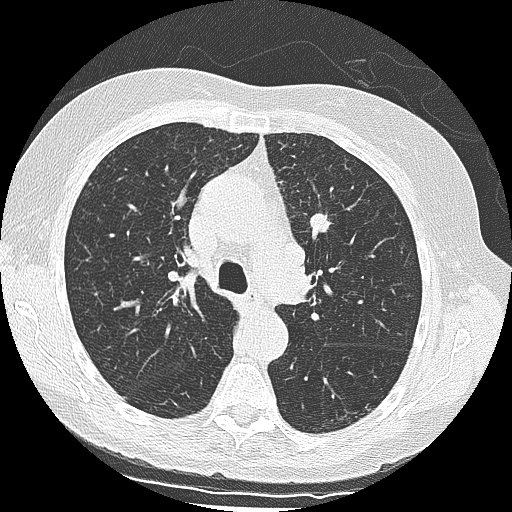
Low-dose screening chest CT, one axial slice; position 95 of 139 along the scan axis; reconstruction kernel LUNG; lung window (W 1500 / L -600 HU); 2.5 mm slice thickness; 512 × 512 image matrix, field of view 318 × 318 mm.
Outlined on this slice (manually delineated by an expert):
- lesion 1 (tumor, upper lobe of left lung): bounding box (x1, y1, x2, y2) in pixels: (309, 213, 334, 240)